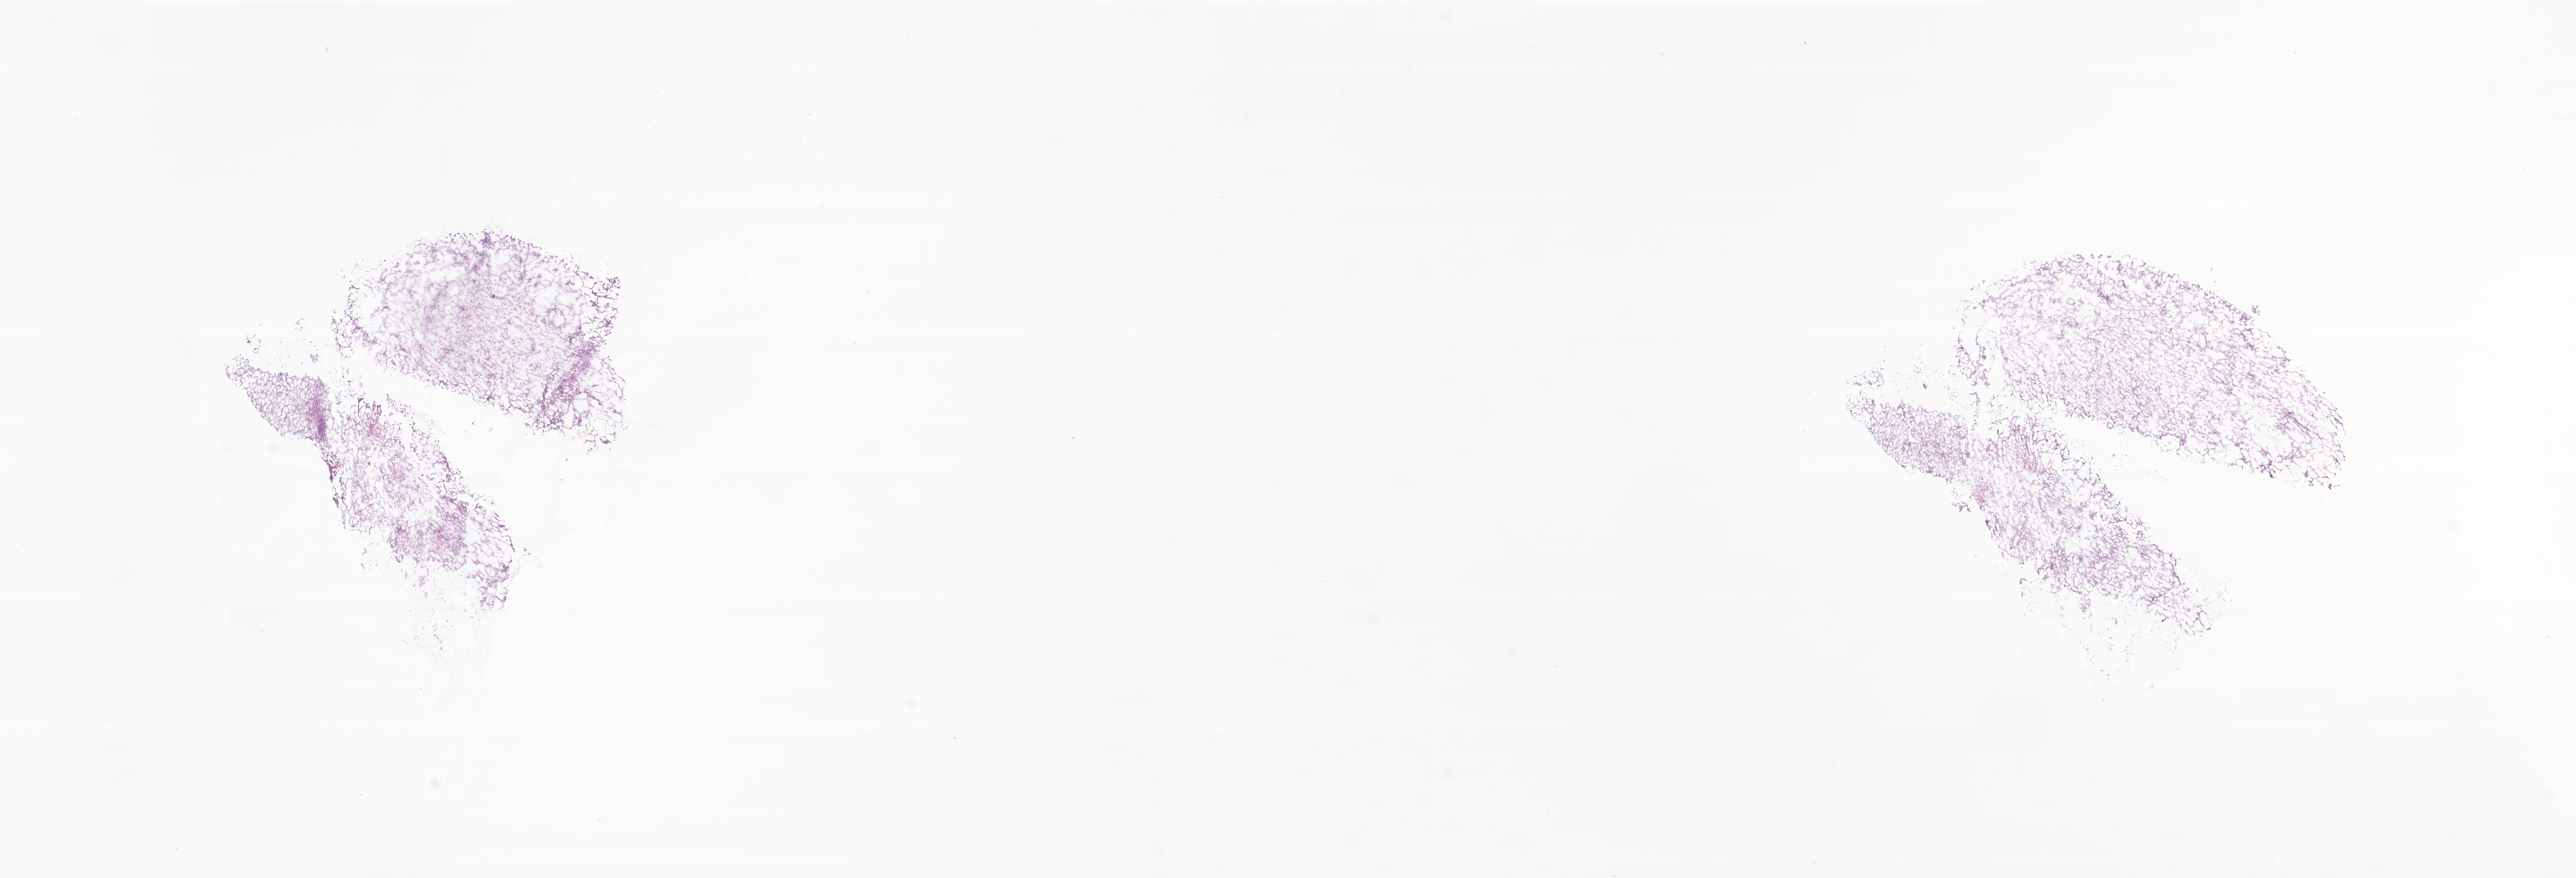
Whole-slide image, H&E stain of tumor tissue from the brain stem, shown as a low-resolution overview of the whole scanned area (about 20.9 x 7.1 mm), cryosection (OCT / tissue freezing medium). Patient female; age 53 months.
- diagnosis: Pilocytic astrocytoma